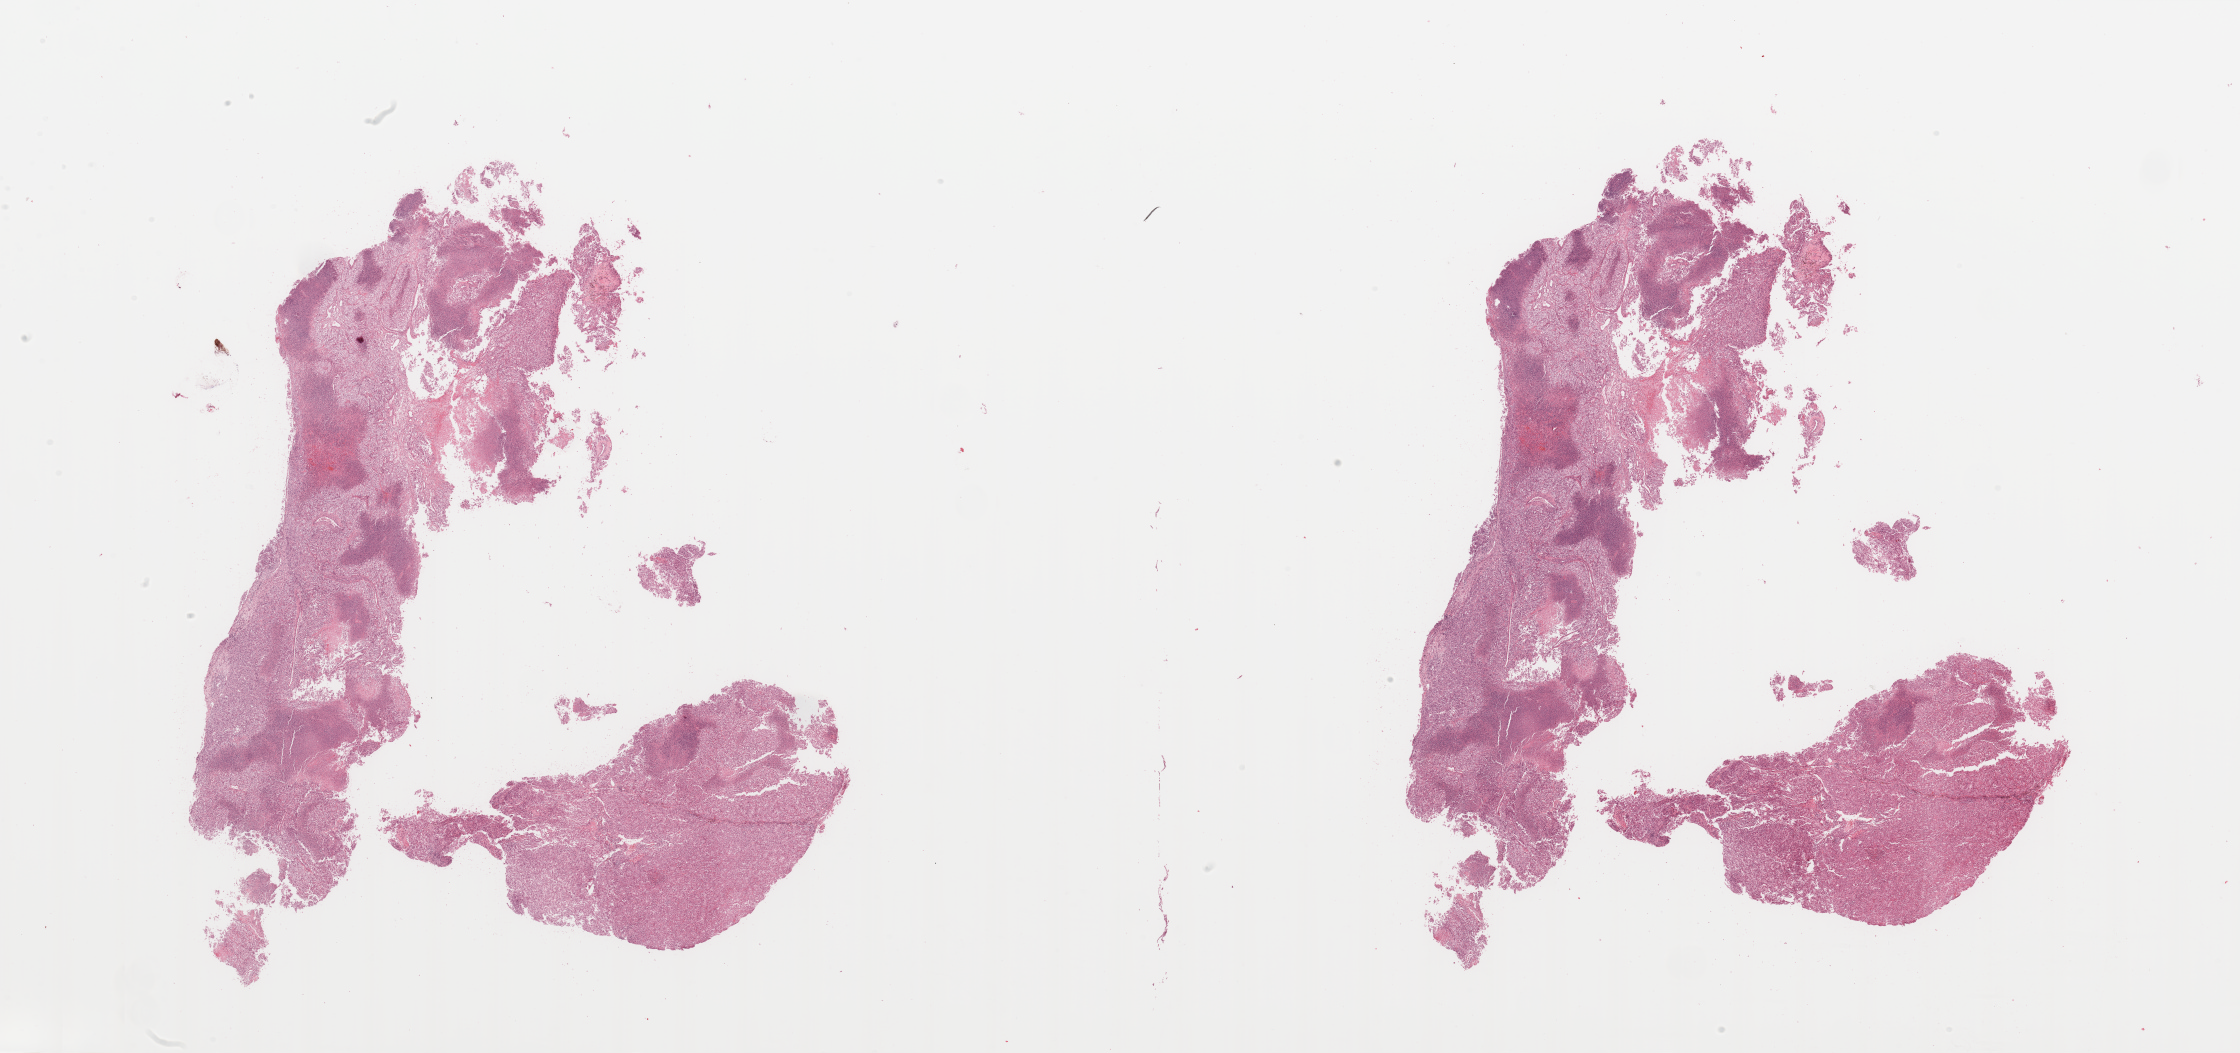
Whole-slide histology image, H&E-stained — low-resolution overview of the scanned area, about 35.4 x 16.7 mm; tumour tissue sample, kidney. Male, 57 y/o. Histologic grade: G4 (undifferentiated).
AJCC pathologic stage: III. Histologic diagnosis: Renal cell carcinoma, NOS.